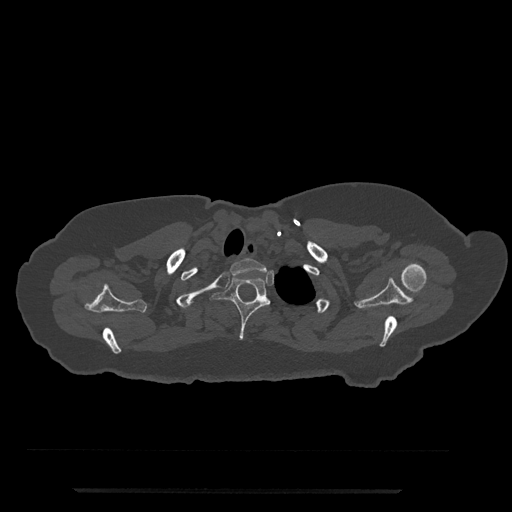
CT including the spine, one axial slice; position 678 of 797 along the scan axis; bone window (W 1800 / L 400 HU); 0.5 mm slice thickness; 512 × 512 image matrix, field of view 440 × 440 mm. Female patient, age 51 years. Case-level facts recorded for this patient, not image findings: primary cancer: neuro; vertebrae with lytic lesions (as recorded): T8.
Outlined on this slice (semi-automatic segmentation, software-assisted and operator-edited):
- T1 vertebra: bounding box [x1, y1, x2, y2] px = [230, 258, 267, 274]
- T2 vertebra: [211, 275, 270, 340]